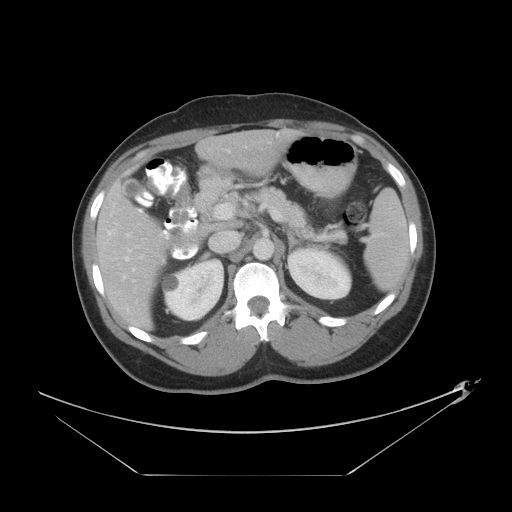
Contrast-enhanced abdominal CT, one axial slice. Slice 24 of 44 in the series (ordered by position). Reconstruction kernel STANDARD. 120 kVp. Soft-tissue window (W 400 / L 40 HU). 5 mm slice thickness. 512 × 512 image matrix. Male patient, age 49 years. From the clinical record (not read from this slice): diagnosis: colorectal cancer liver metastases, imaged before liver resection; multiple liver metastases: no; largest metastasis: 8.5 cm; disease in both lobes: yes.
Annotated regions visible in this slice (expert manual segmentation):
- hepatic veins: bounding box [x1, y1, x2, y2] px = [125, 149, 230, 261]
- liver: [97, 130, 301, 330]
- planned liver remnant (the part of the liver to remain after resection): [229, 130, 301, 175]
- portal vein (with intrahepatic branches): [108, 203, 234, 271]